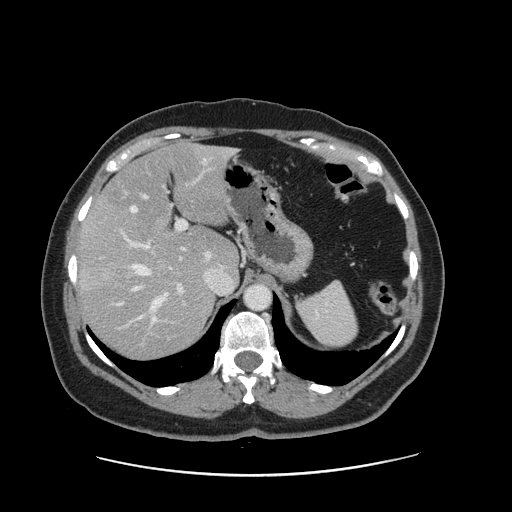
Contrast-enhanced abdominal CT, one axial slice; position 105 of 161 along the scan axis; 120 kVp; soft-tissue window (W 400 / L 40 HU); 512 × 512 image matrix. Female patient, age 62 years. From the clinical record (not read from this slice): diagnosis: colorectal cancer liver metastases, imaged before liver resection; multiple liver metastases: no; largest metastasis: 2.5 cm; chemotherapy before resection: yes.
Outlined on this slice (manually delineated by an expert):
- hepatic veins: bounding box [x1, y1, x2, y2] px = [131, 149, 236, 321]
- liver: [81, 144, 238, 359]
- planned liver remnant (the part of the liver to remain after resection): [101, 145, 238, 275]
- portal vein (with intrahepatic branches): [112, 170, 203, 334]
- liver metastasis: [112, 267, 127, 281]